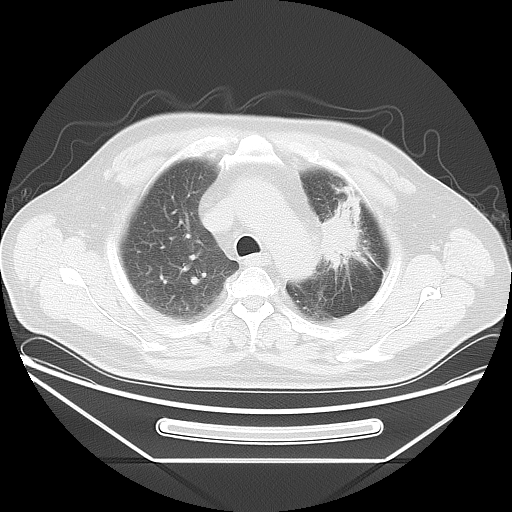
Chest CT, one axial slice. Slice 30 of 37 in the series (ordered by position). Reconstruction kernel LUNG. 120 kVp. Lung window (W 1500 / L -600 HU). 5 mm slice thickness. 512 × 512 image matrix, field of view 411 × 411 mm. Male patient, age 61 years. From the clinical record (not read from this slice): clinical TNM (as recorded): T2a N0 M0; histopathological grade: G3.
Annotated regions visible in this slice (bounding box drawn by a radiologist):
- lung tumour (recorded histology: small cell carcinoma): bounding box <309,175,388,281> (left, top, right, bottom; pixels)